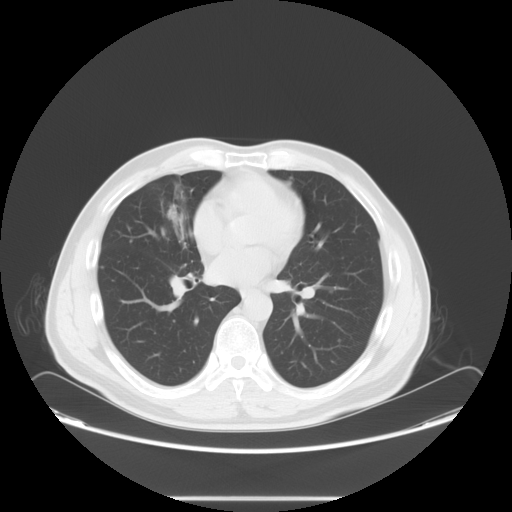
Chest CT, one axial slice; position 37 of 73 along the scan axis; 120 kVp; lung window (W 1500 / L -600 HU); 5 mm slice thickness; 512 × 512 image matrix, field of view 429 × 429 mm. Male patient, age 47 years. Case-level facts recorded for this patient, not image findings: clinical TNM (as recorded): T1c N3 M0.
Annotated regions visible in this slice (rectangle marked by the reading radiologist):
- lung tumour (recorded histology: adenocarcinoma): box from (x=157, y=177) to (x=194, y=224) px